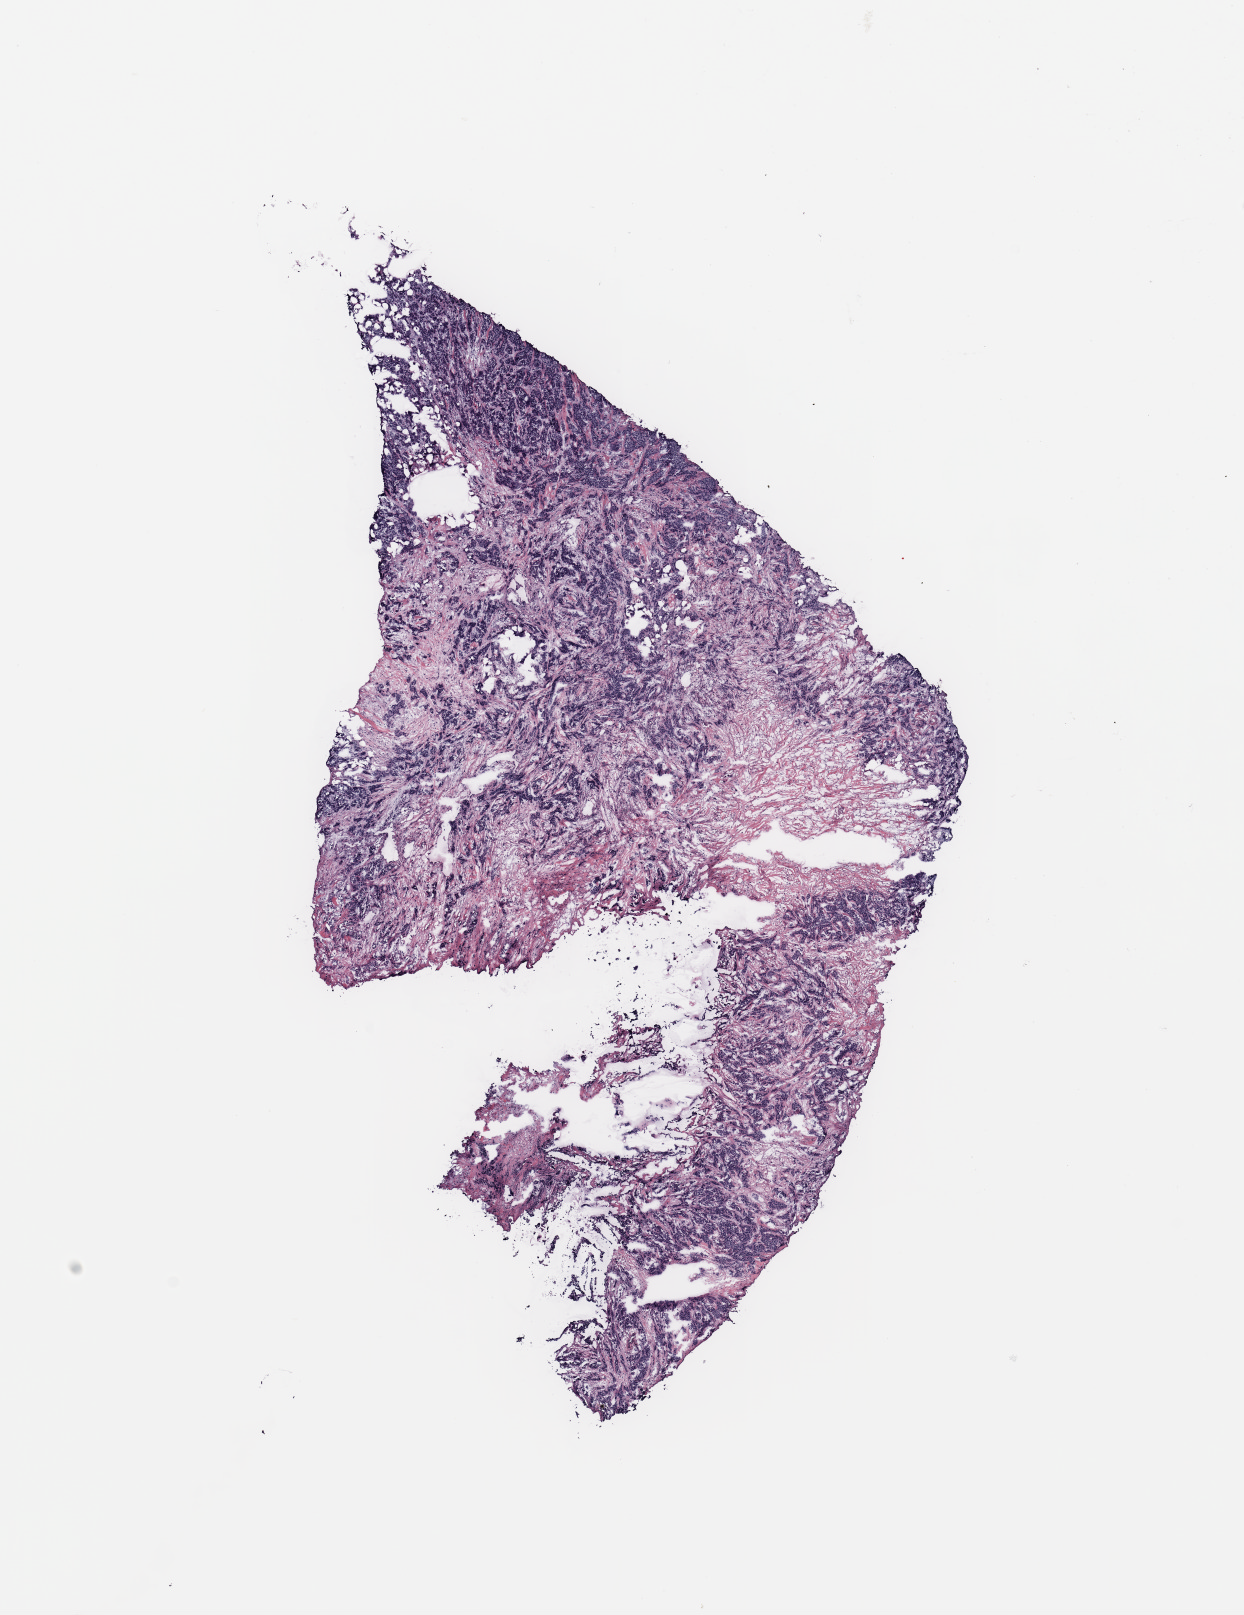
H&E whole-slide image, whole scanned area (about 9.8 x 12.8 mm, from a 20x scan) shown as a low-resolution overview; tumour tissue sample, breast. Female, 60 y/o.
* AJCC pathologic stage: IIA
* diagnosis: Infiltrating duct carcinoma, NOS